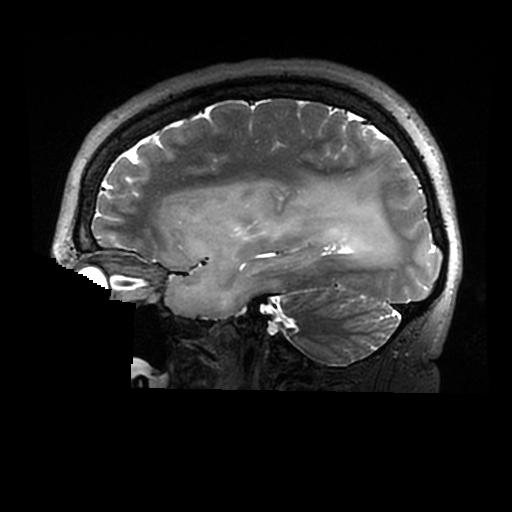
Brain MRI from a brain-tumour surgery series, one sagittal slice. Slice 200 of 320 in the series (ordered by position). 0.6 mm slice thickness. 512 × 512 image matrix. Case-level facts recorded for this patient, not image findings: histopathology: Astrocytoma; WHO grade: 2; IDH mutation: yes.
Outlined on this slice (outlined manually by an expert reader):
- tumour: bounding box <165,181,398,319> (left, top, right, bottom; pixels)